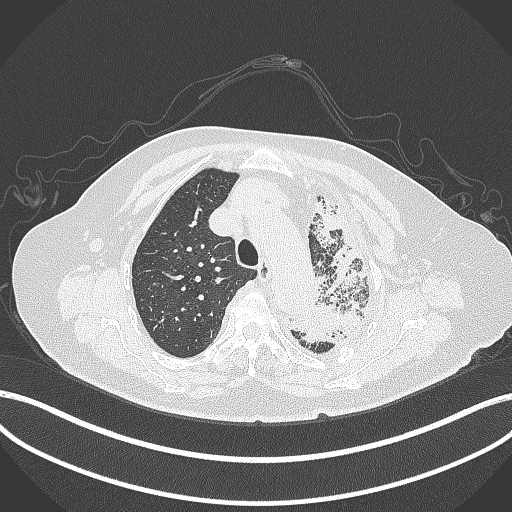
Chest CT, one axial slice; position 301 of 399 along the scan axis; reconstruction kernel B70f; lung window (W 1500 / L -600 HU); 1 mm slice thickness; 512 × 512 image matrix, field of view 400 × 400 mm. Patient: female, 75 years. Case-level facts recorded for this patient, not image findings: clinical TNM (as recorded): T3 N3 M1.
Annotated regions visible in this slice (bounding box drawn by a radiologist):
- lung tumour (recorded histology: adenocarcinoma): box from (x=290, y=201) to (x=371, y=349) px